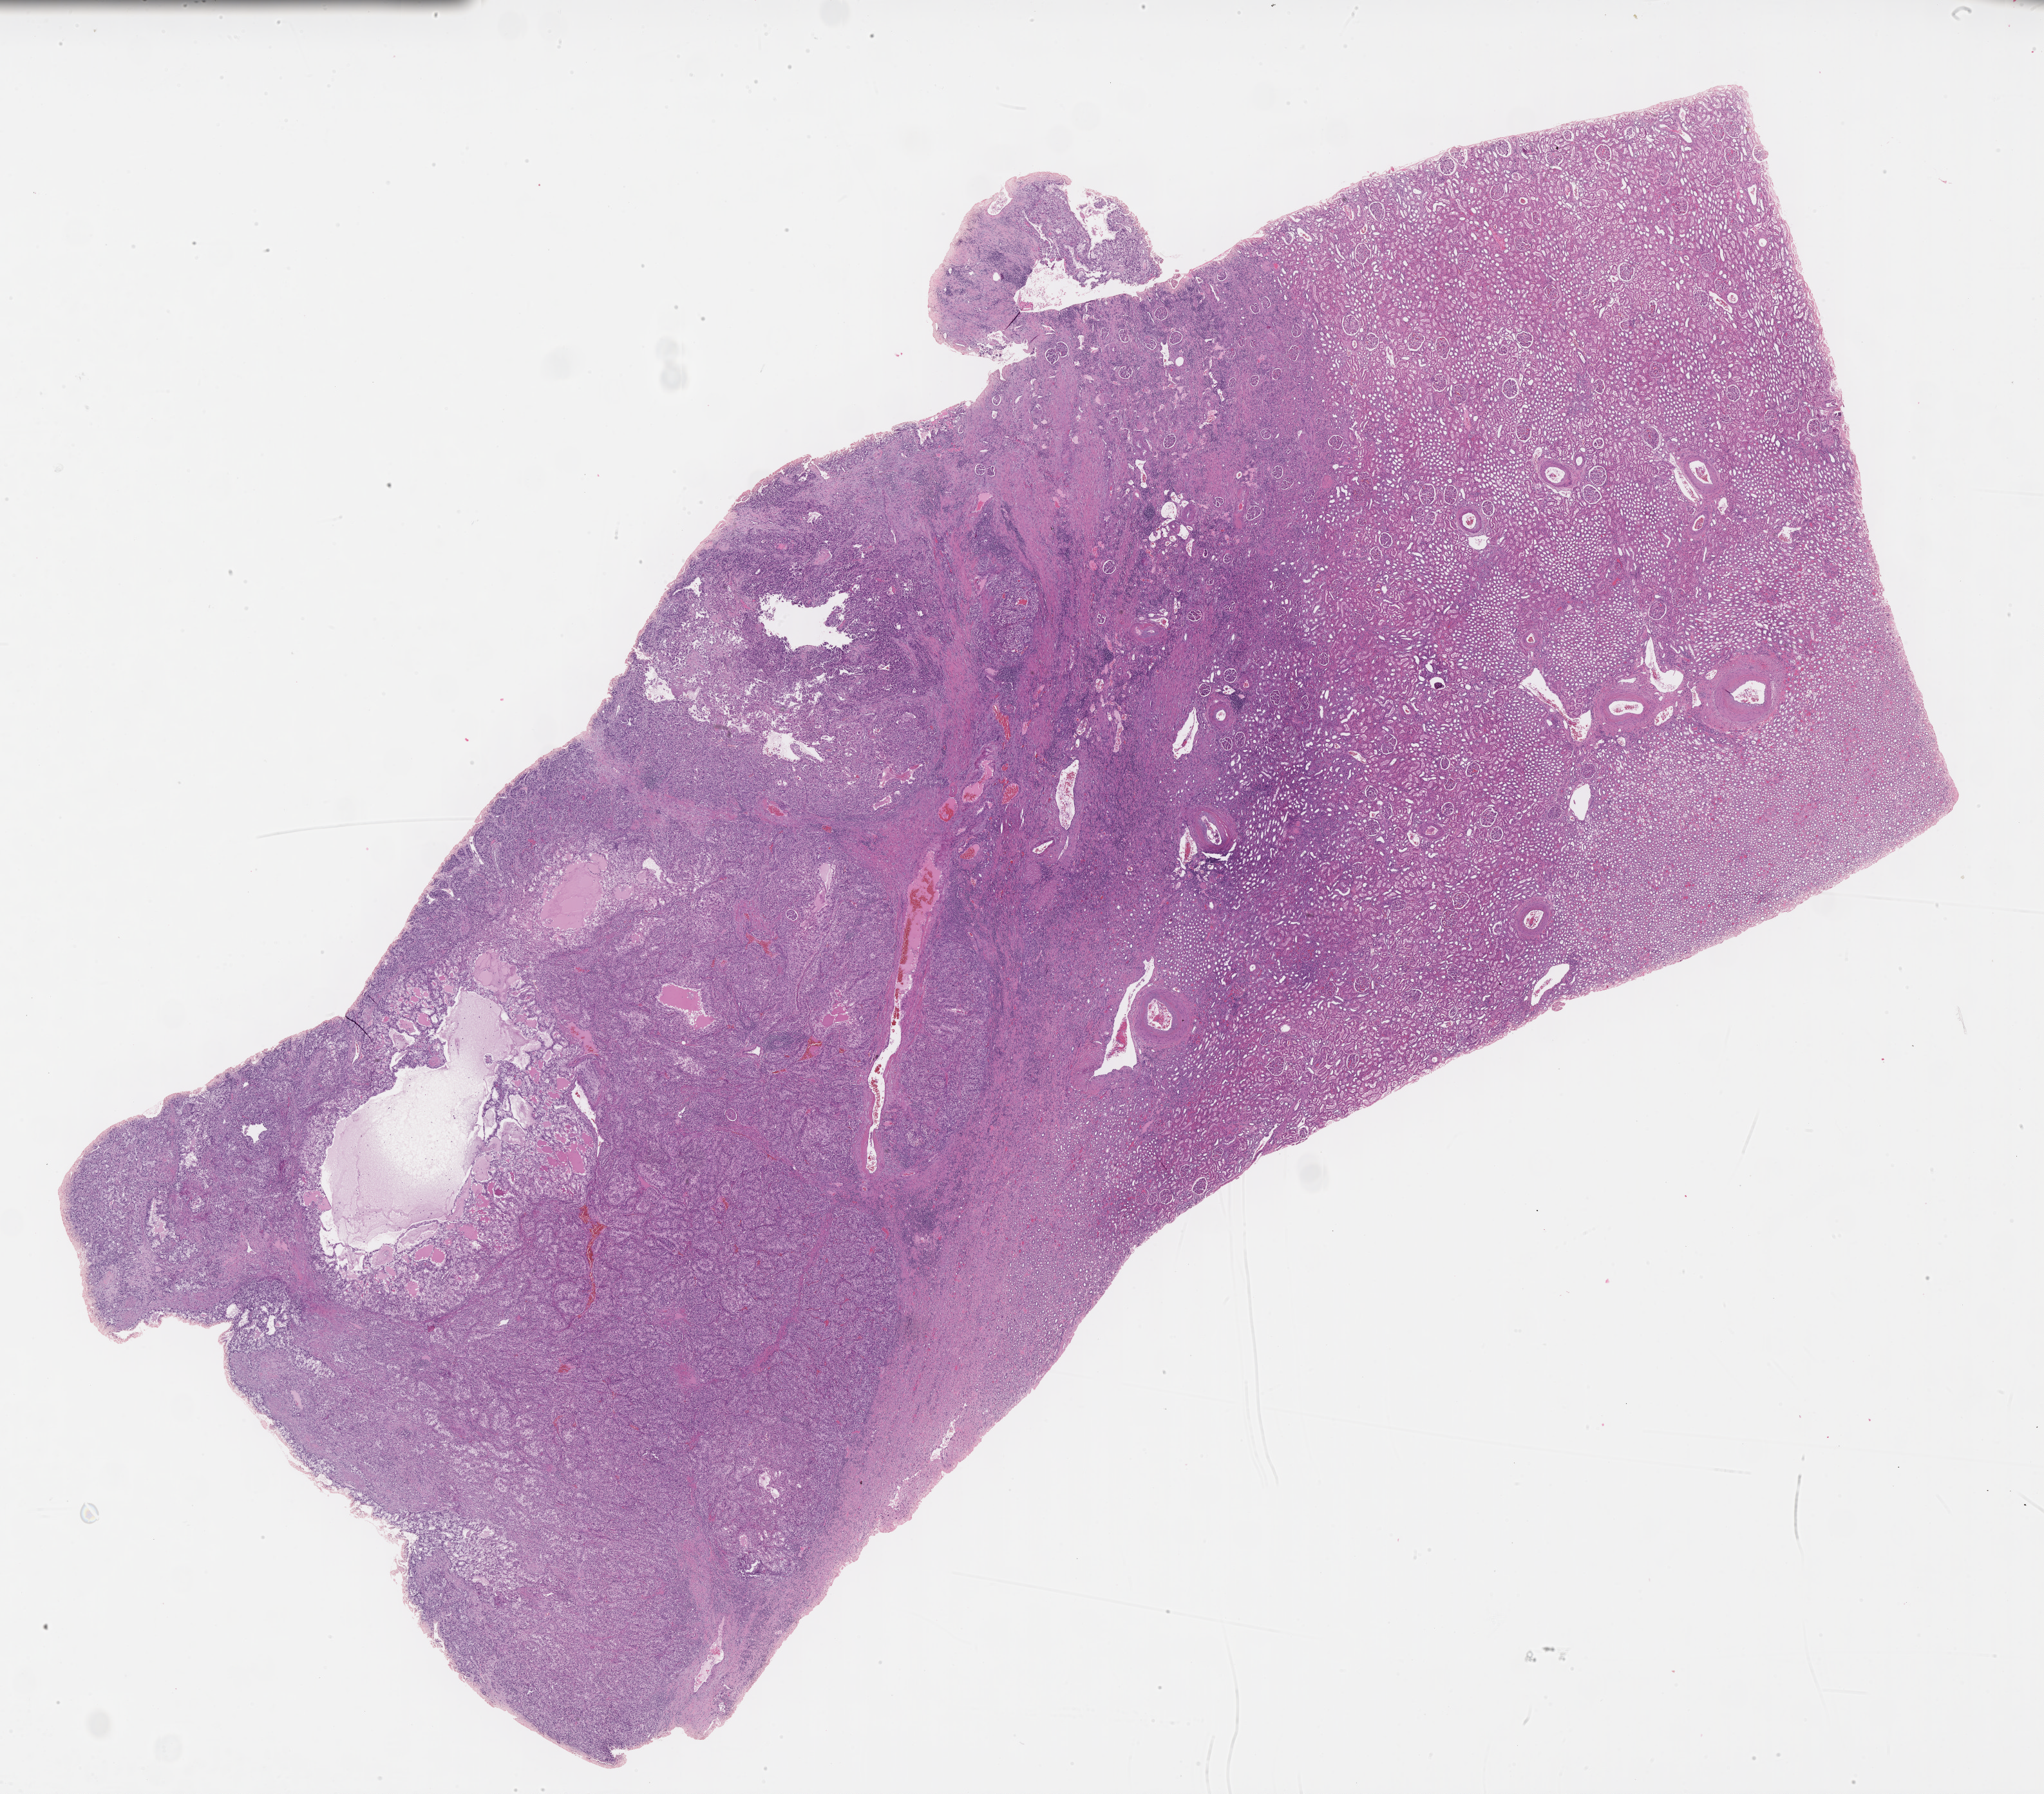
H&E whole-slide image — shown as a low-resolution overview of the whole scanned area (about 25.7 x 22.5 mm, acquisition: 40x scan), formalin-fixed paraffin-embedded (FFPE) diagnostic section, primary tumour sample from the kidney. Patient: male, age at initial diagnosis 57 years. Histologic grade: G3 (poorly differentiated).
TNM: T3a NX M0. AJCC pathologic stage: III. Histologic diagnosis: Clear cell adenocarcinoma, NOS.